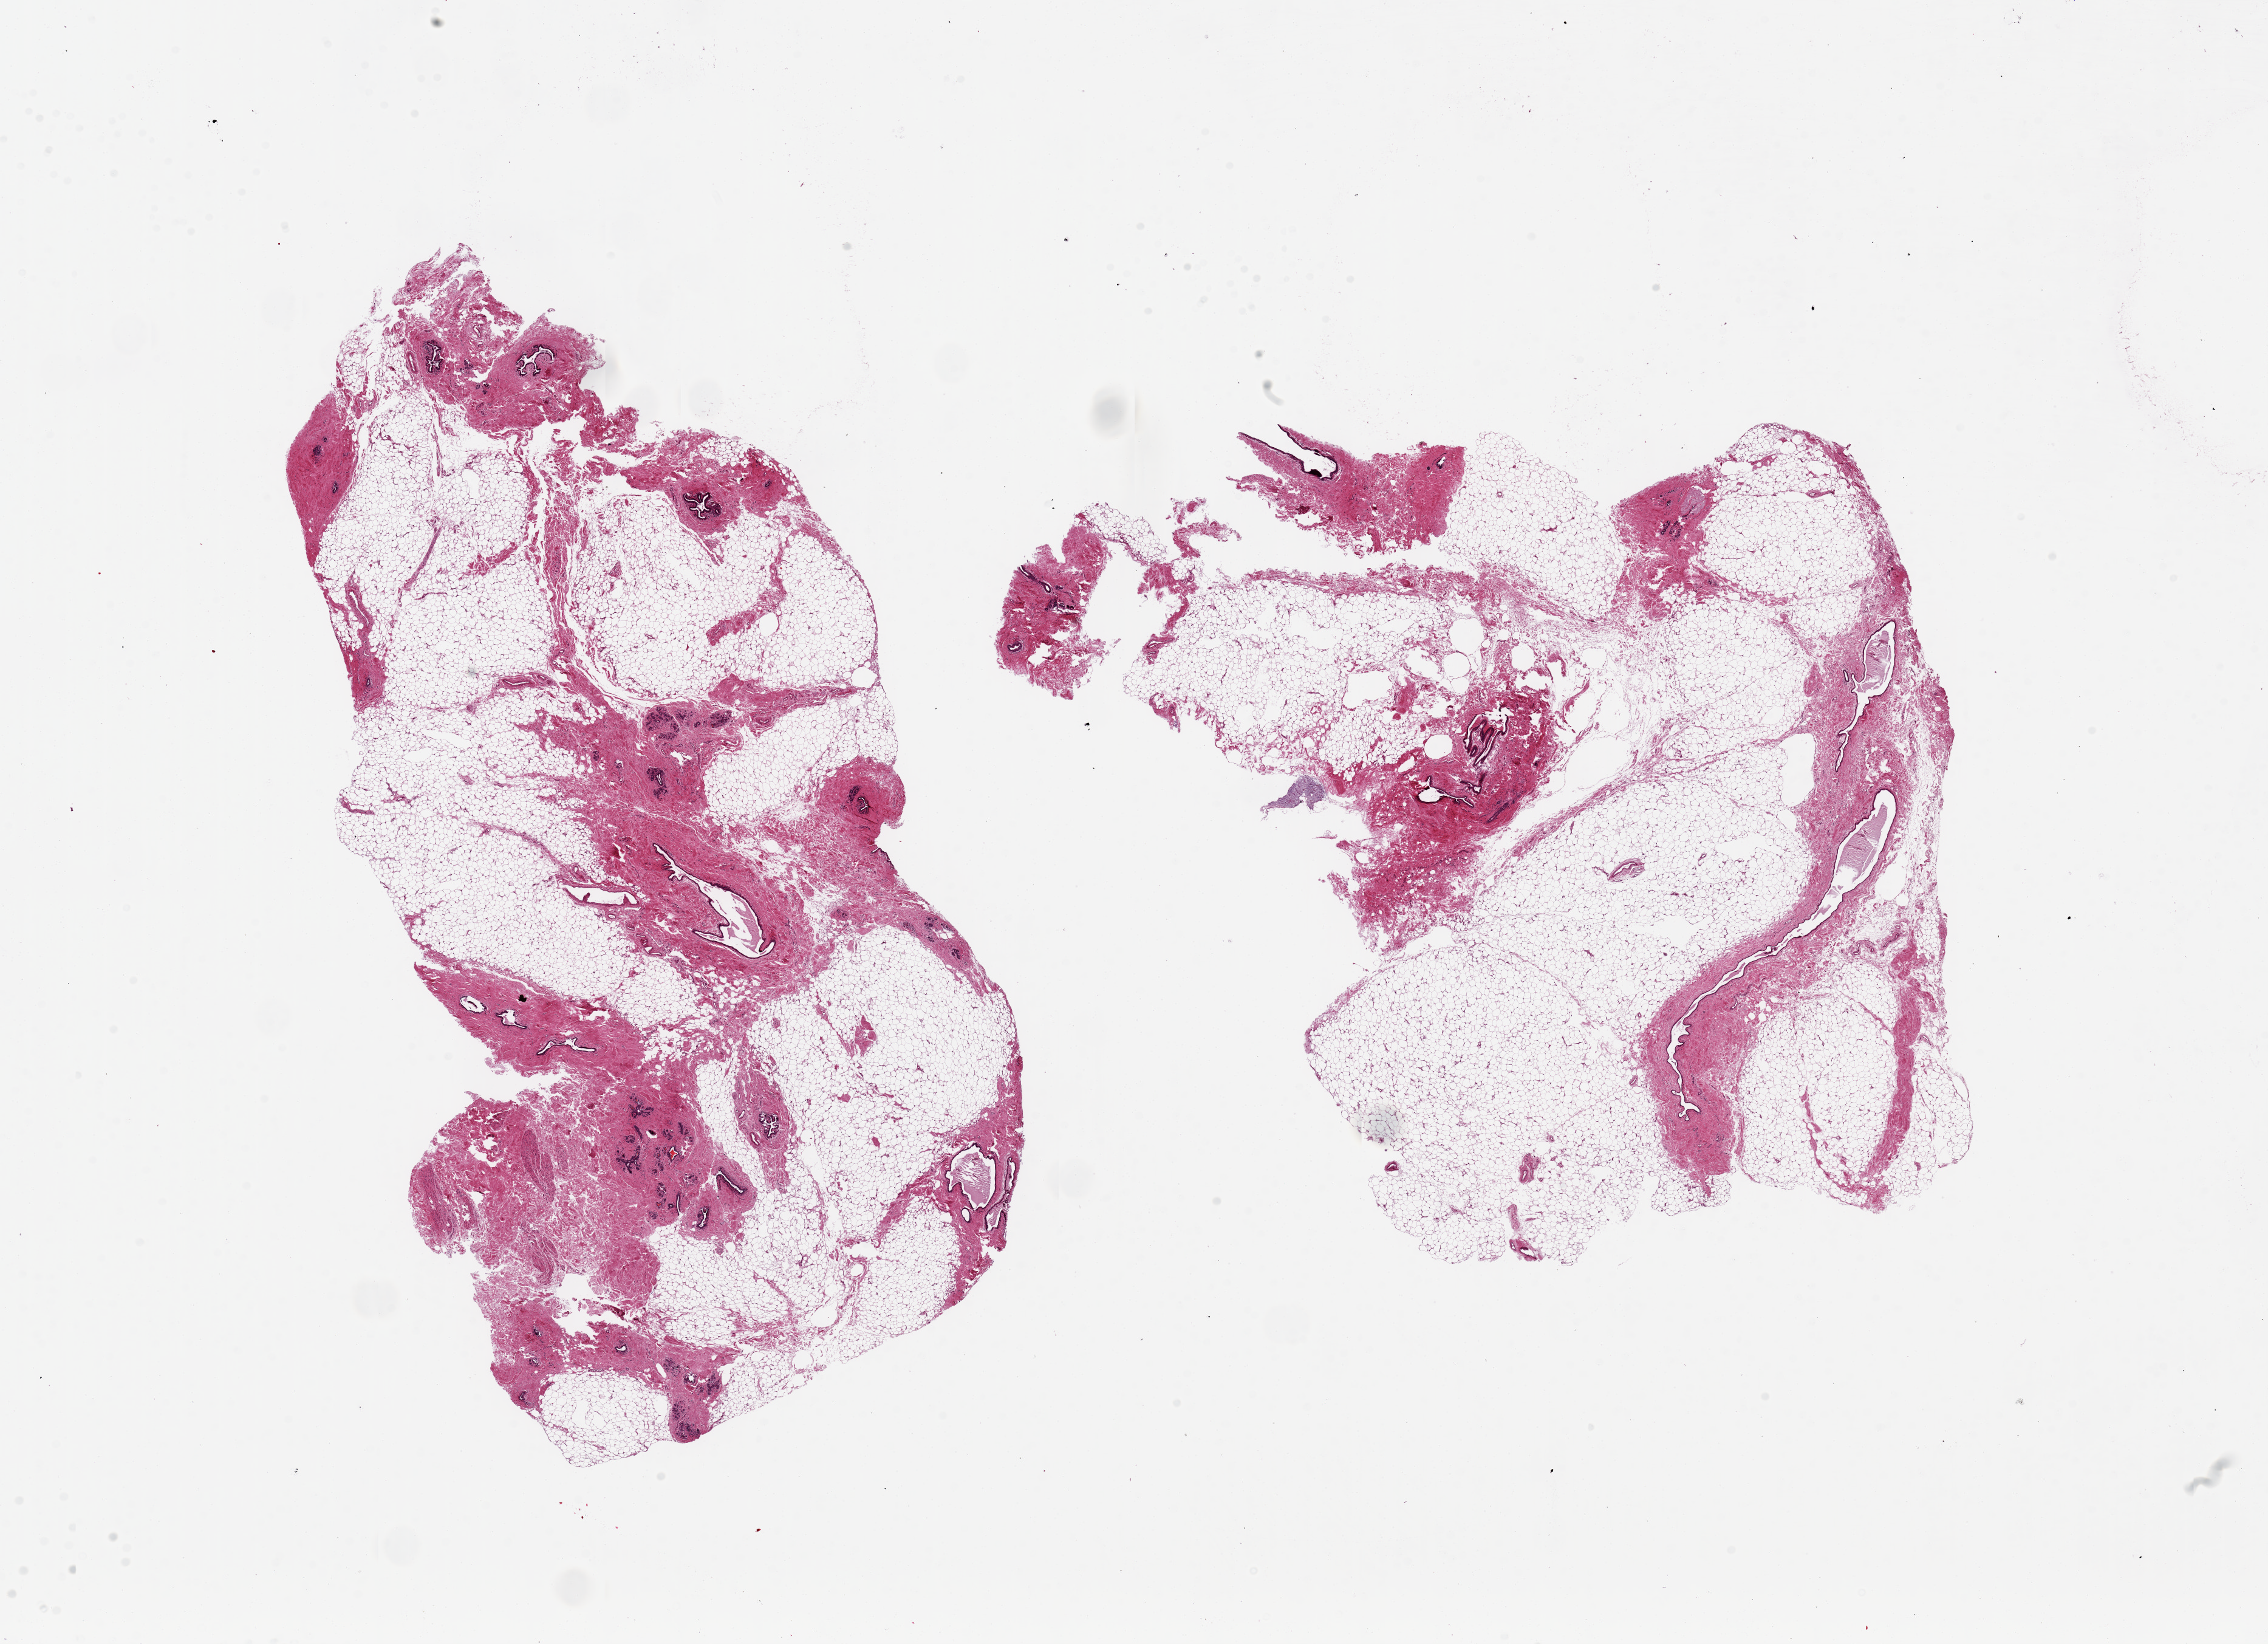
Hematoxylin and eosin (H&E) whole-slide image — whole scanned area (about 29.5 x 21.4 mm) shown as a low-resolution overview; PAXgene-fixed, paraffin-embedded tissue; section of breast (target tissue); donor tissue sample. Female donor.
Review note (as recorded): 2 pieces, 15x8 & 12x11.5mm; ductal/lobular units.